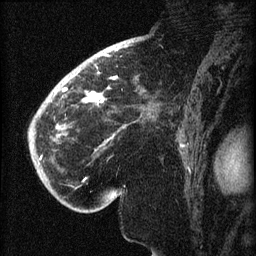
Breast MRI (dynamic contrast-enhanced), one sagittal slice; slice 47 of 60 in the series (ordered by position); dynamic contrast-enhanced series, image 2 of 3 at this slice position (ordered by acquisition); 1.5 T; TE 4.2 ms, TR 8.2 ms; 256 × 256 image matrix, field of view 180 × 180 mm. Patient: female, 71 years.
Outlined on this slice (semi-automatic segmentation, software-assisted and operator-edited):
- analysis volume of interest (the breast-tissue region the enhancement analysis was run in; not a lesion): bounding box <40,72,148,196> (left, top, right, bottom; pixels)
- tumour enhancement mask (voxels above the 70 % enhancement threshold inside the analysis volume of interest): <40,87,105,160>